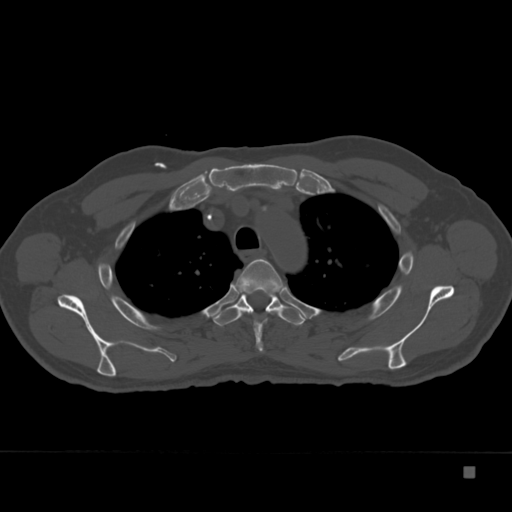
CT including the spine, one axial slice; bone window (W 1800 / L 400 HU); 1.5 mm slice thickness; 512 × 512 image matrix. Male patient, age 72 years. From the clinical record (not read from this slice): primary cancer: skeletal.
Structures marked on this image (semi-automatic segmentation, software-assisted and operator-edited):
- T3 vertebra: bounding box <235,258,285,352> (left, top, right, bottom; pixels)
- T4 vertebra: <213,295,306,326>